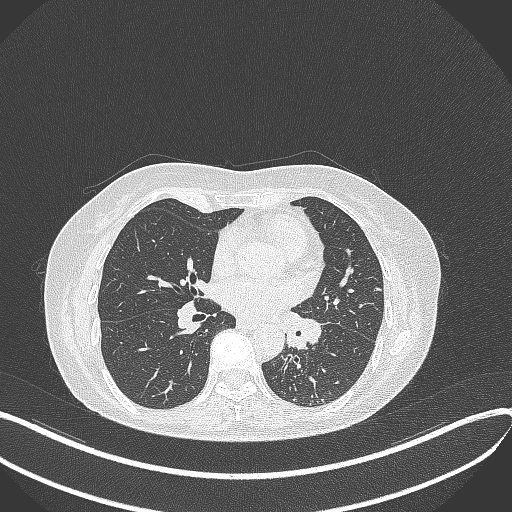
Chest CT, one axial slice. Position 199 of 429 along the scan axis. Reconstruction kernel B70f. 100 kVp. Lung window (W 1500 / L -600 HU). 512 × 512 image matrix, field of view 400 × 400 mm. Female patient, age 63 years. From the clinical record (not read from this slice): clinical TNM (as recorded): T1b N0 M0; histopathological grade: G2-3.
Annotated regions visible in this slice (rectangle marked by the reading radiologist):
- lung tumour (recorded histology: adenocarcinoma): bounding box (x1, y1, x2, y2) in pixels: (281, 311, 331, 361)